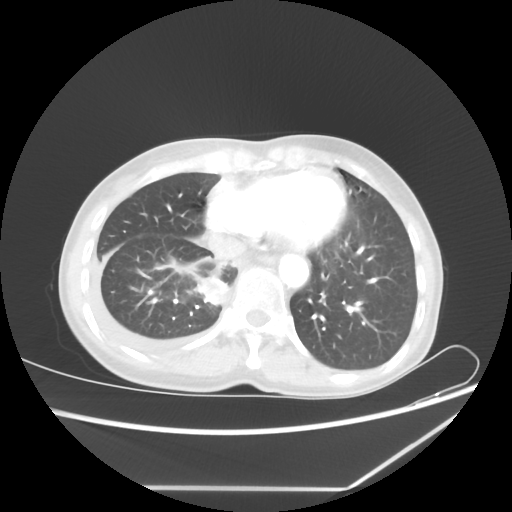
Chest CT, one axial slice; slice 17 of 60 in the series (ordered by position); reconstruction kernel STANDARD; 80 kVp; lung window (W 1500 / L -600 HU); 5 mm slice thickness; 512 × 512 image matrix, field of view 364 × 364 mm. Patient: female, 59 years. Case-level facts recorded for this patient, not image findings: clinical TNM (as recorded): T1c N1 M1.
Annotated regions visible in this slice (bounding box drawn by a radiologist):
- lung tumour (recorded histology: adenocarcinoma): box from (x=196, y=273) to (x=230, y=307) px